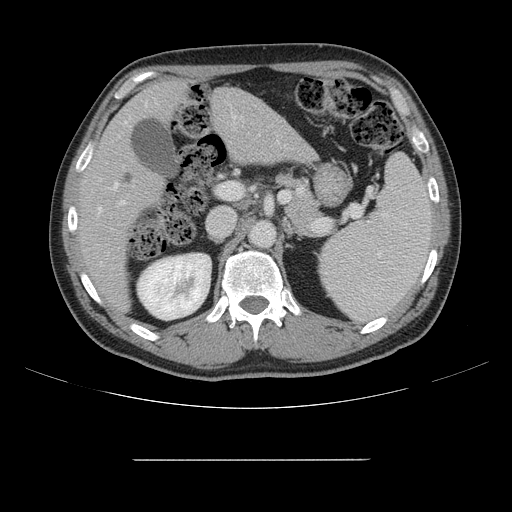
Contrast-enhanced abdominal CT, one axial slice; position 87 of 164 along the scan axis; intravenous contrast given; soft-tissue window (W 400 / L 40 HU); 2.5 mm slice thickness; 512 × 512 image matrix, field of view 404 × 404 mm. Male patient, age 54 years. From the clinical record (not read from this slice): diagnosis: colorectal cancer liver metastases, imaged before liver resection; multiple liver metastases: yes; largest metastasis: 1 cm; disease in both lobes: no.
Outlined on this slice (manually delineated by an expert):
- hepatic veins: bounding box (x1, y1, x2, y2) in pixels: (98, 182, 119, 212)
- liver: (81, 81, 311, 307)
- planned liver remnant (the part of the liver to remain after resection): (81, 81, 229, 307)
- portal vein (with intrahepatic branches): (120, 122, 260, 205)